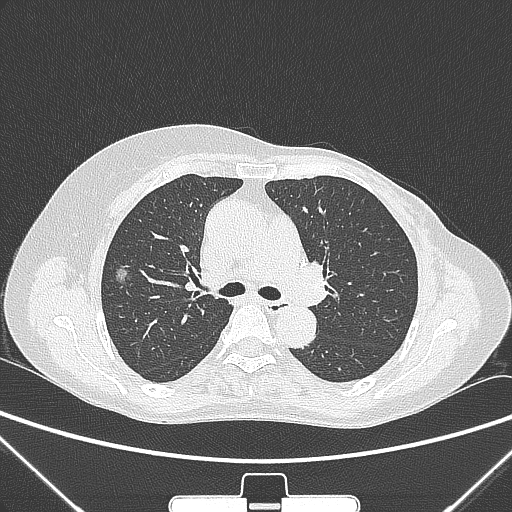
Chest CT, one axial slice; slice 162 of 265 in the series (ordered by position); 120 kVp; lung window (W 1500 / L -600 HU); 1 mm slice thickness; 512 × 512 image matrix, field of view 350 × 350 mm. Female patient, age 64 years. From the clinical record (not read from this slice): clinical TNM (as recorded): T1c N0 M0; histopathological grade: G1-2.
Outlined on this slice (rectangle marked by the reading radiologist):
- lung tumour (recorded histology: adenocarcinoma): bounding box [x1, y1, x2, y2] px = [110, 258, 131, 288]